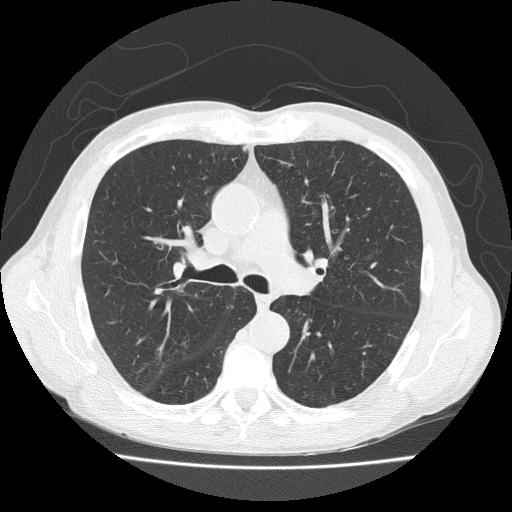
Low-dose screening chest CT, axial slice, baseline screening round, lung window (W 1500 / L -600 HU), 2 mm slice thickness, lung (sharp) reconstruction kernel (FC51), 120 kVp, slice 78 of 203 in the series, 512 × 512 image matrix, field of view 370 × 370 mm. Male, age 73 years at enrolment.
Lesion marked by an expert reader, bounding box [x1, y1, x2, y2] px = [143, 328, 190, 374]. No non-calcified nodule or mass ≥4 mm was recorded by the screening reader at this exam. Official screen result: negative screen, no significant abnormalities. Later outcome: lung cancer diagnosed 777 days after this screen (after the third annual screen) — adenosquamous carcinoma, right upper lobe, well differentiated (G1), stage IA (AJCC 6th edition), 20 mm at pathology.